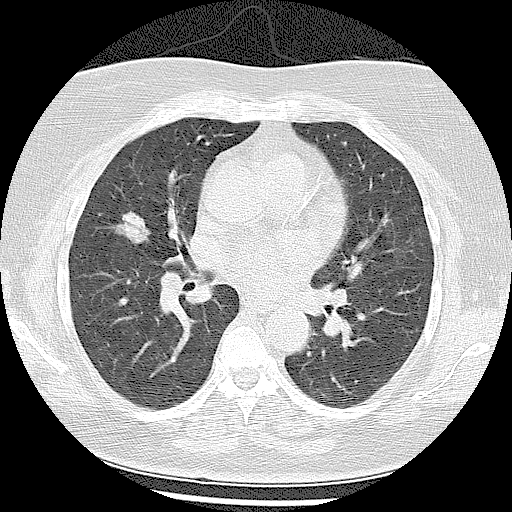
Axial slice from a low-dose chest CT screening exam; first (baseline) screen; lung window (W 1500 / L -600 HU); 2.5 mm slice thickness; lung (sharp) reconstruction kernel (LUNG); slice 51 of 102 in the series; 512 × 512 image matrix, field of view 350 × 350 mm. Female, age 57 years at enrolment. Former smoker at enrolment.
Lesion marked by an expert reader, bounding box [x1, y1, x2, y2] px = [104, 202, 168, 257]. The screening reader recorded 4 non-calcified nodules or masses ≥4 mm on this exam (right middle lobe, right lower lobe, left lower lobe, left lower lobe); which of them this box marks is not recorded. Official screen result: positive, change unspecified: nodule(s) >= 4 mm or enlarging nodule(s), mass(es), or other non-specific abnormalities suspicious for lung cancer.